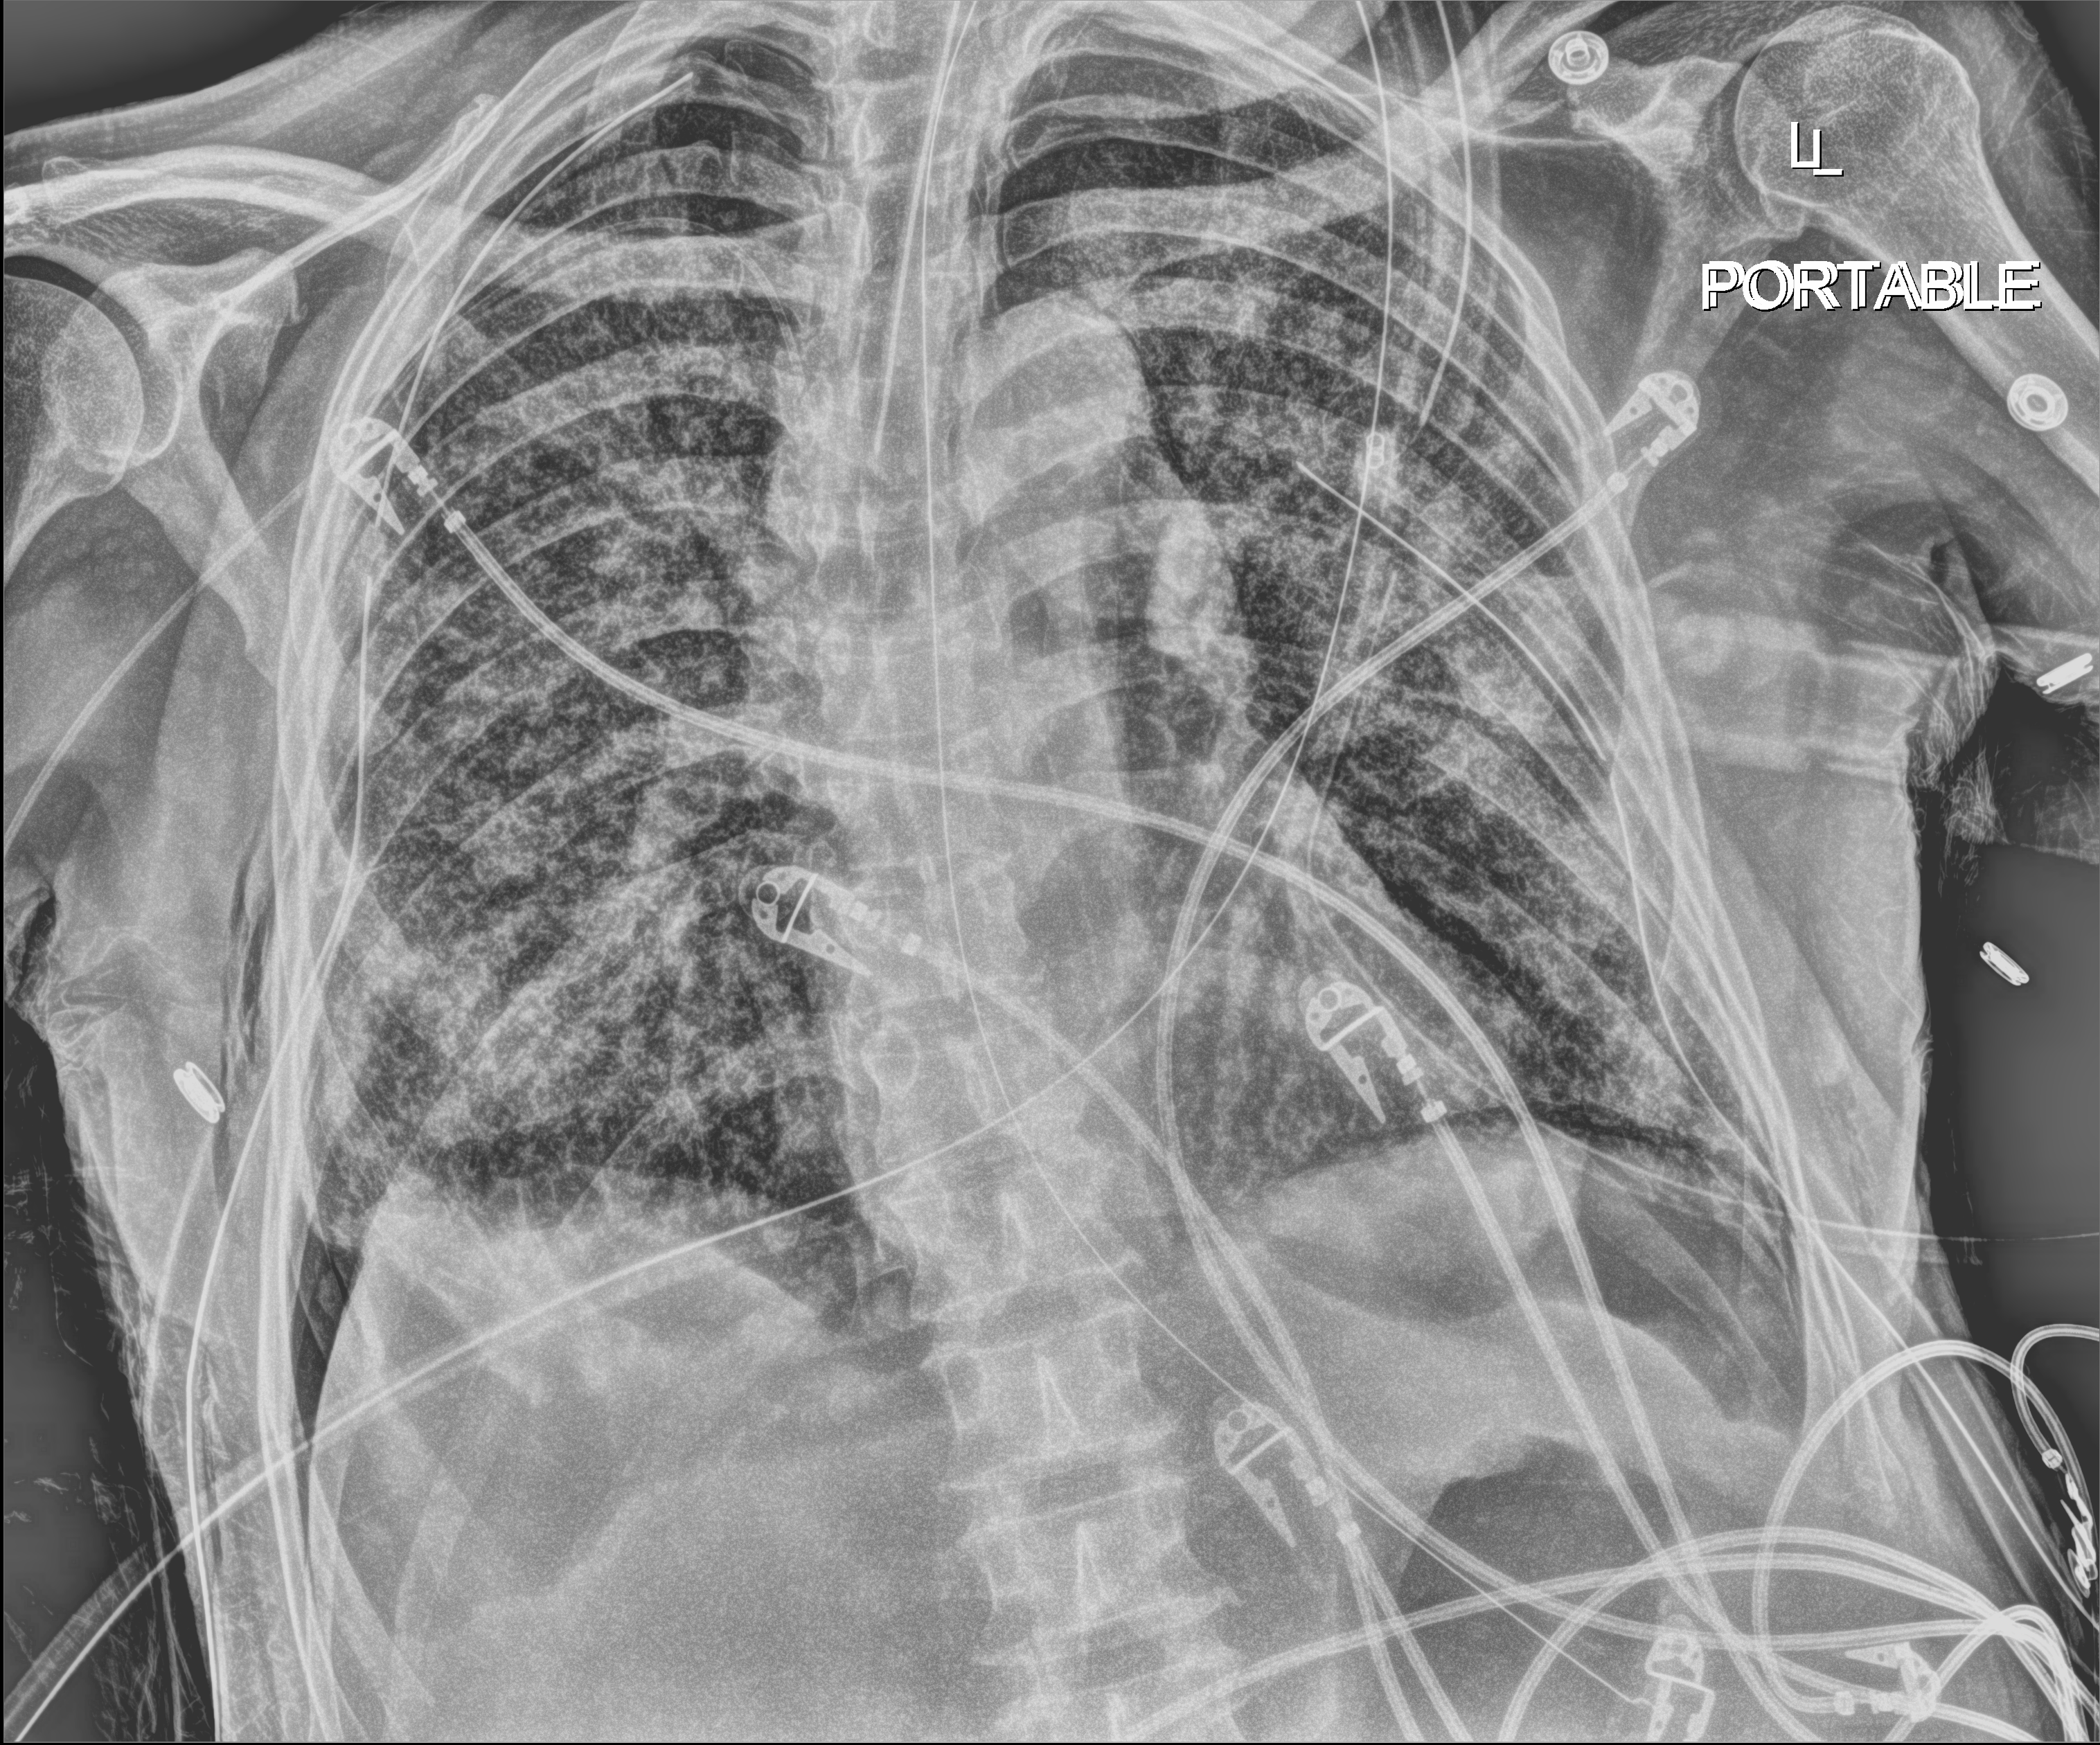
Chest X-ray (portable); anteroposterior (AP) projection. Patient hospitalised with COVID-19; male, aged 60–74 years.
Hospital-stay facts (about this admission, not read from this image; timing relative to this image not recorded): smoking status (admission record): never; mechanically ventilated during this hospital stay: yes.